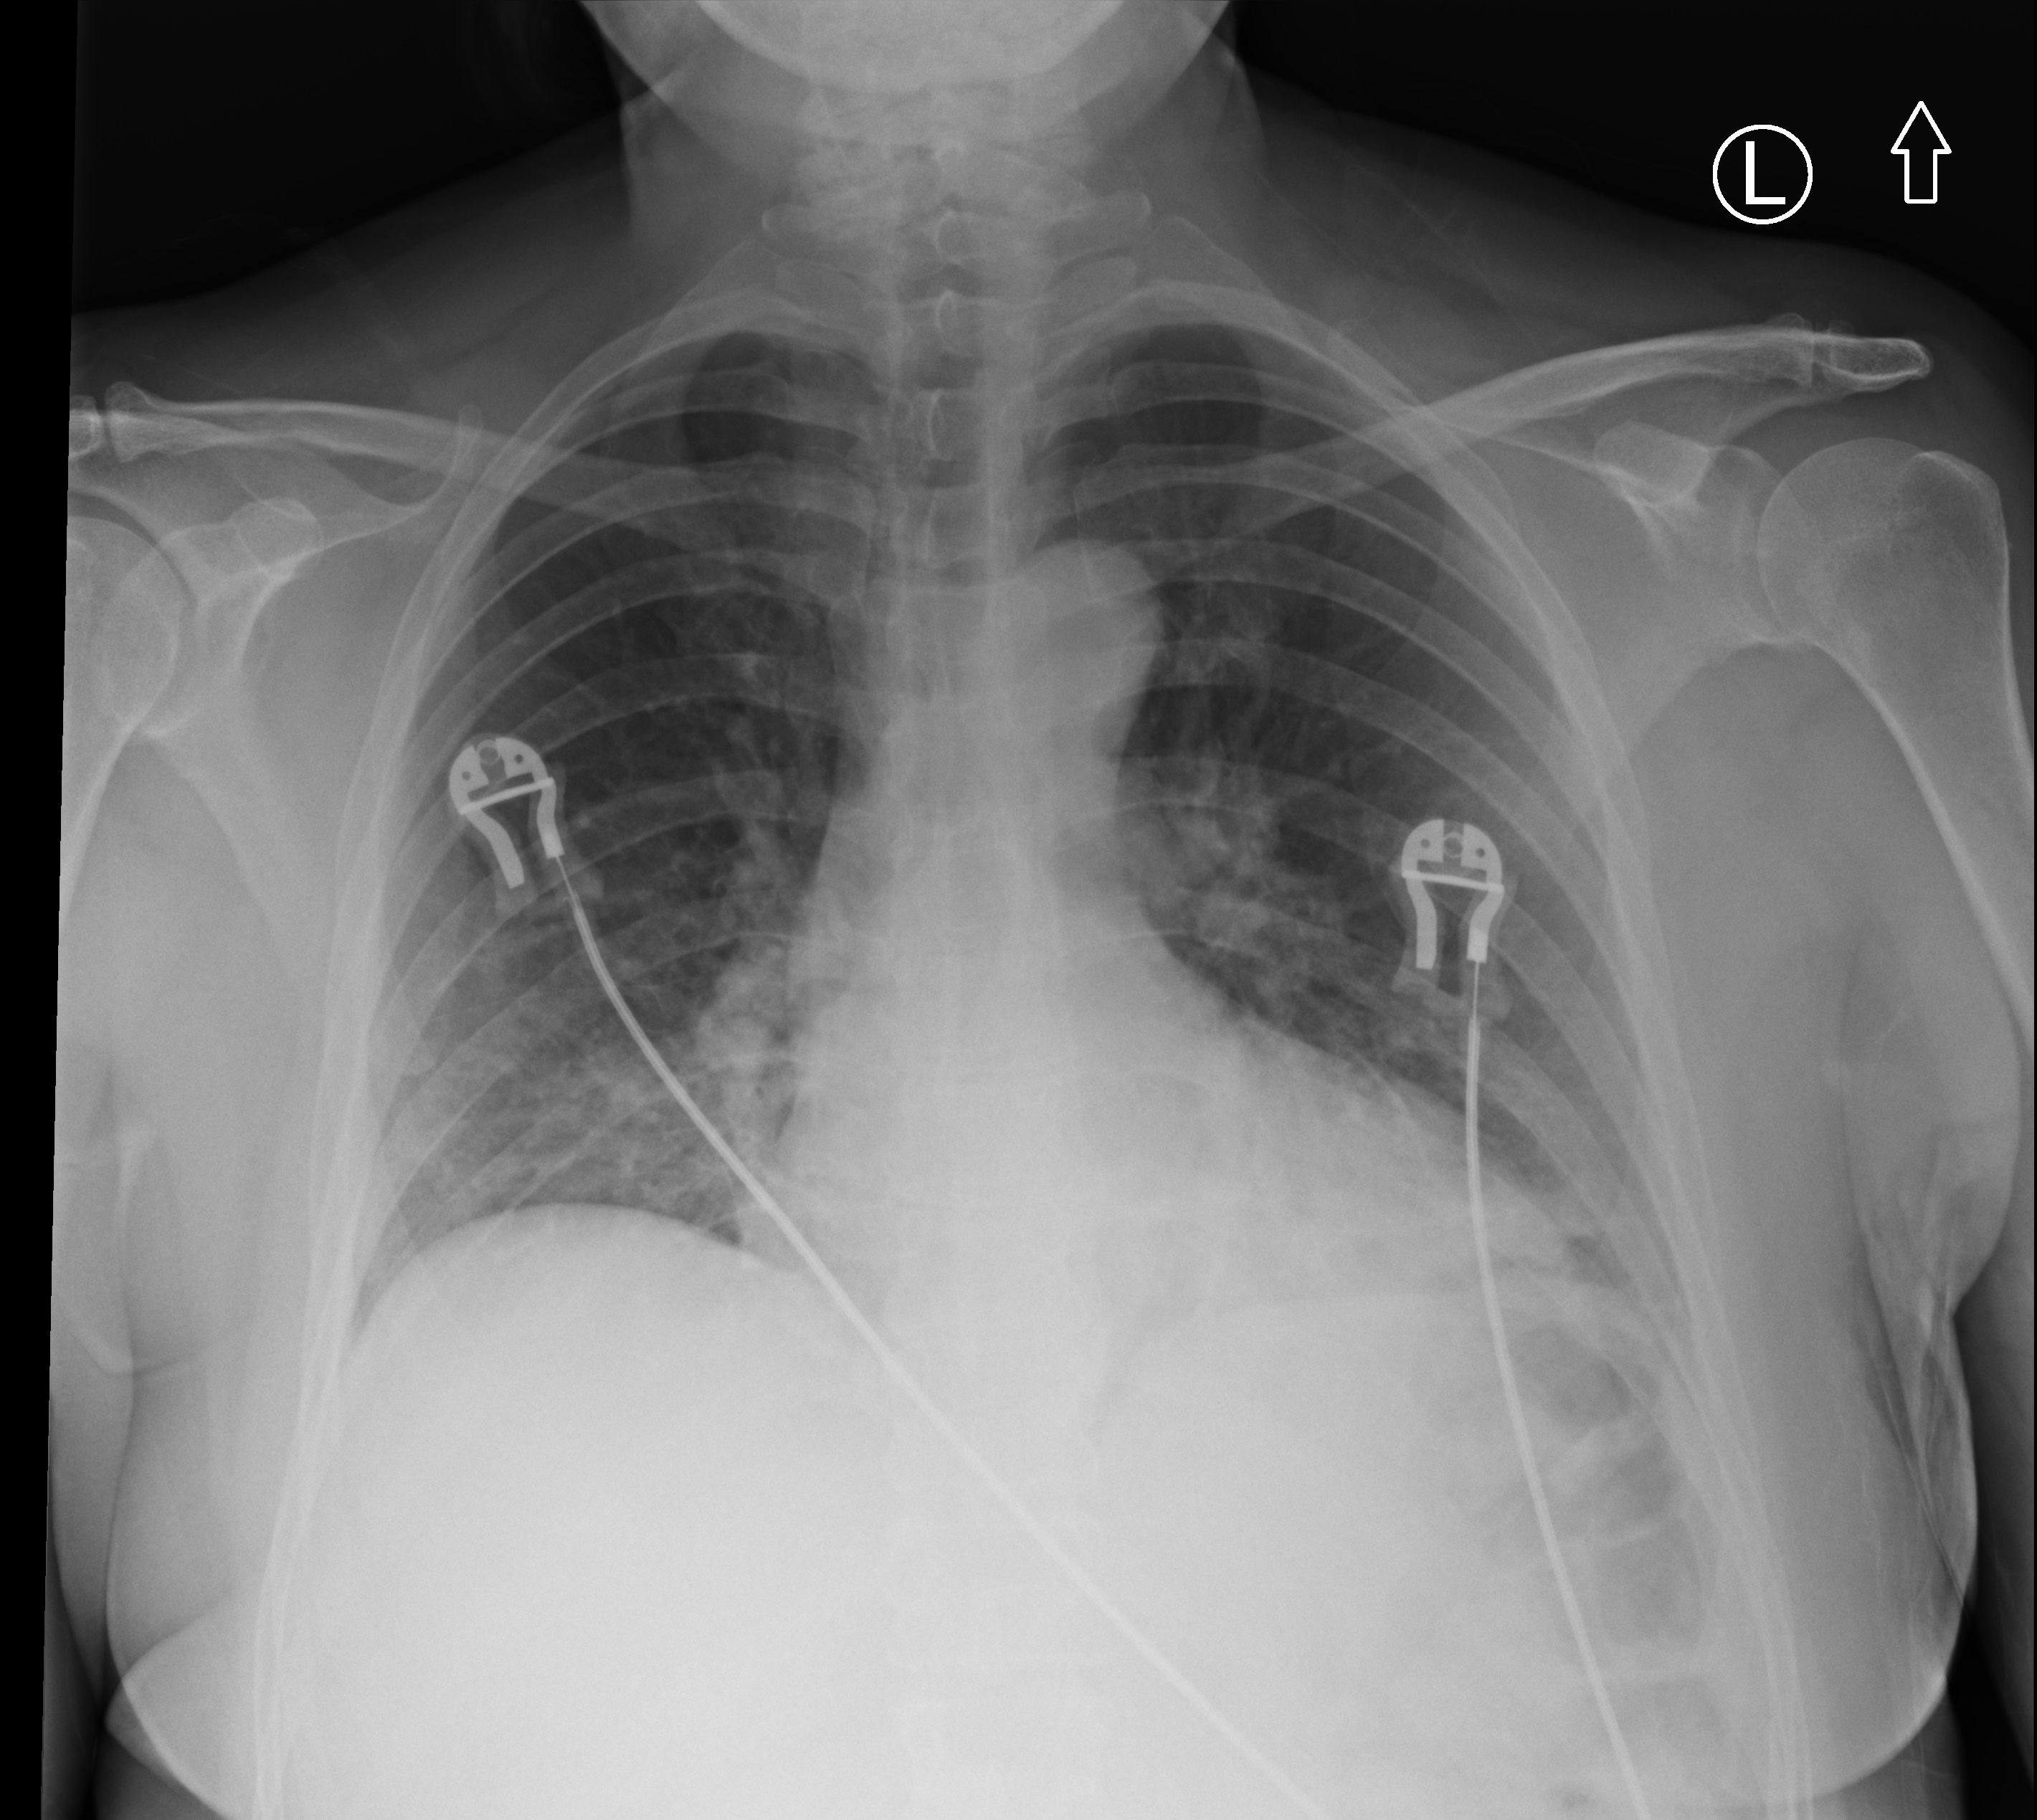
Chest X-ray (portable); anteroposterior (AP) projection. Patient hospitalised with COVID-19; female, aged 18–59 years.
Hospital-stay facts (about this admission, not read from this image; timing relative to this image not recorded): admitted to intensive care during this hospital stay: no.